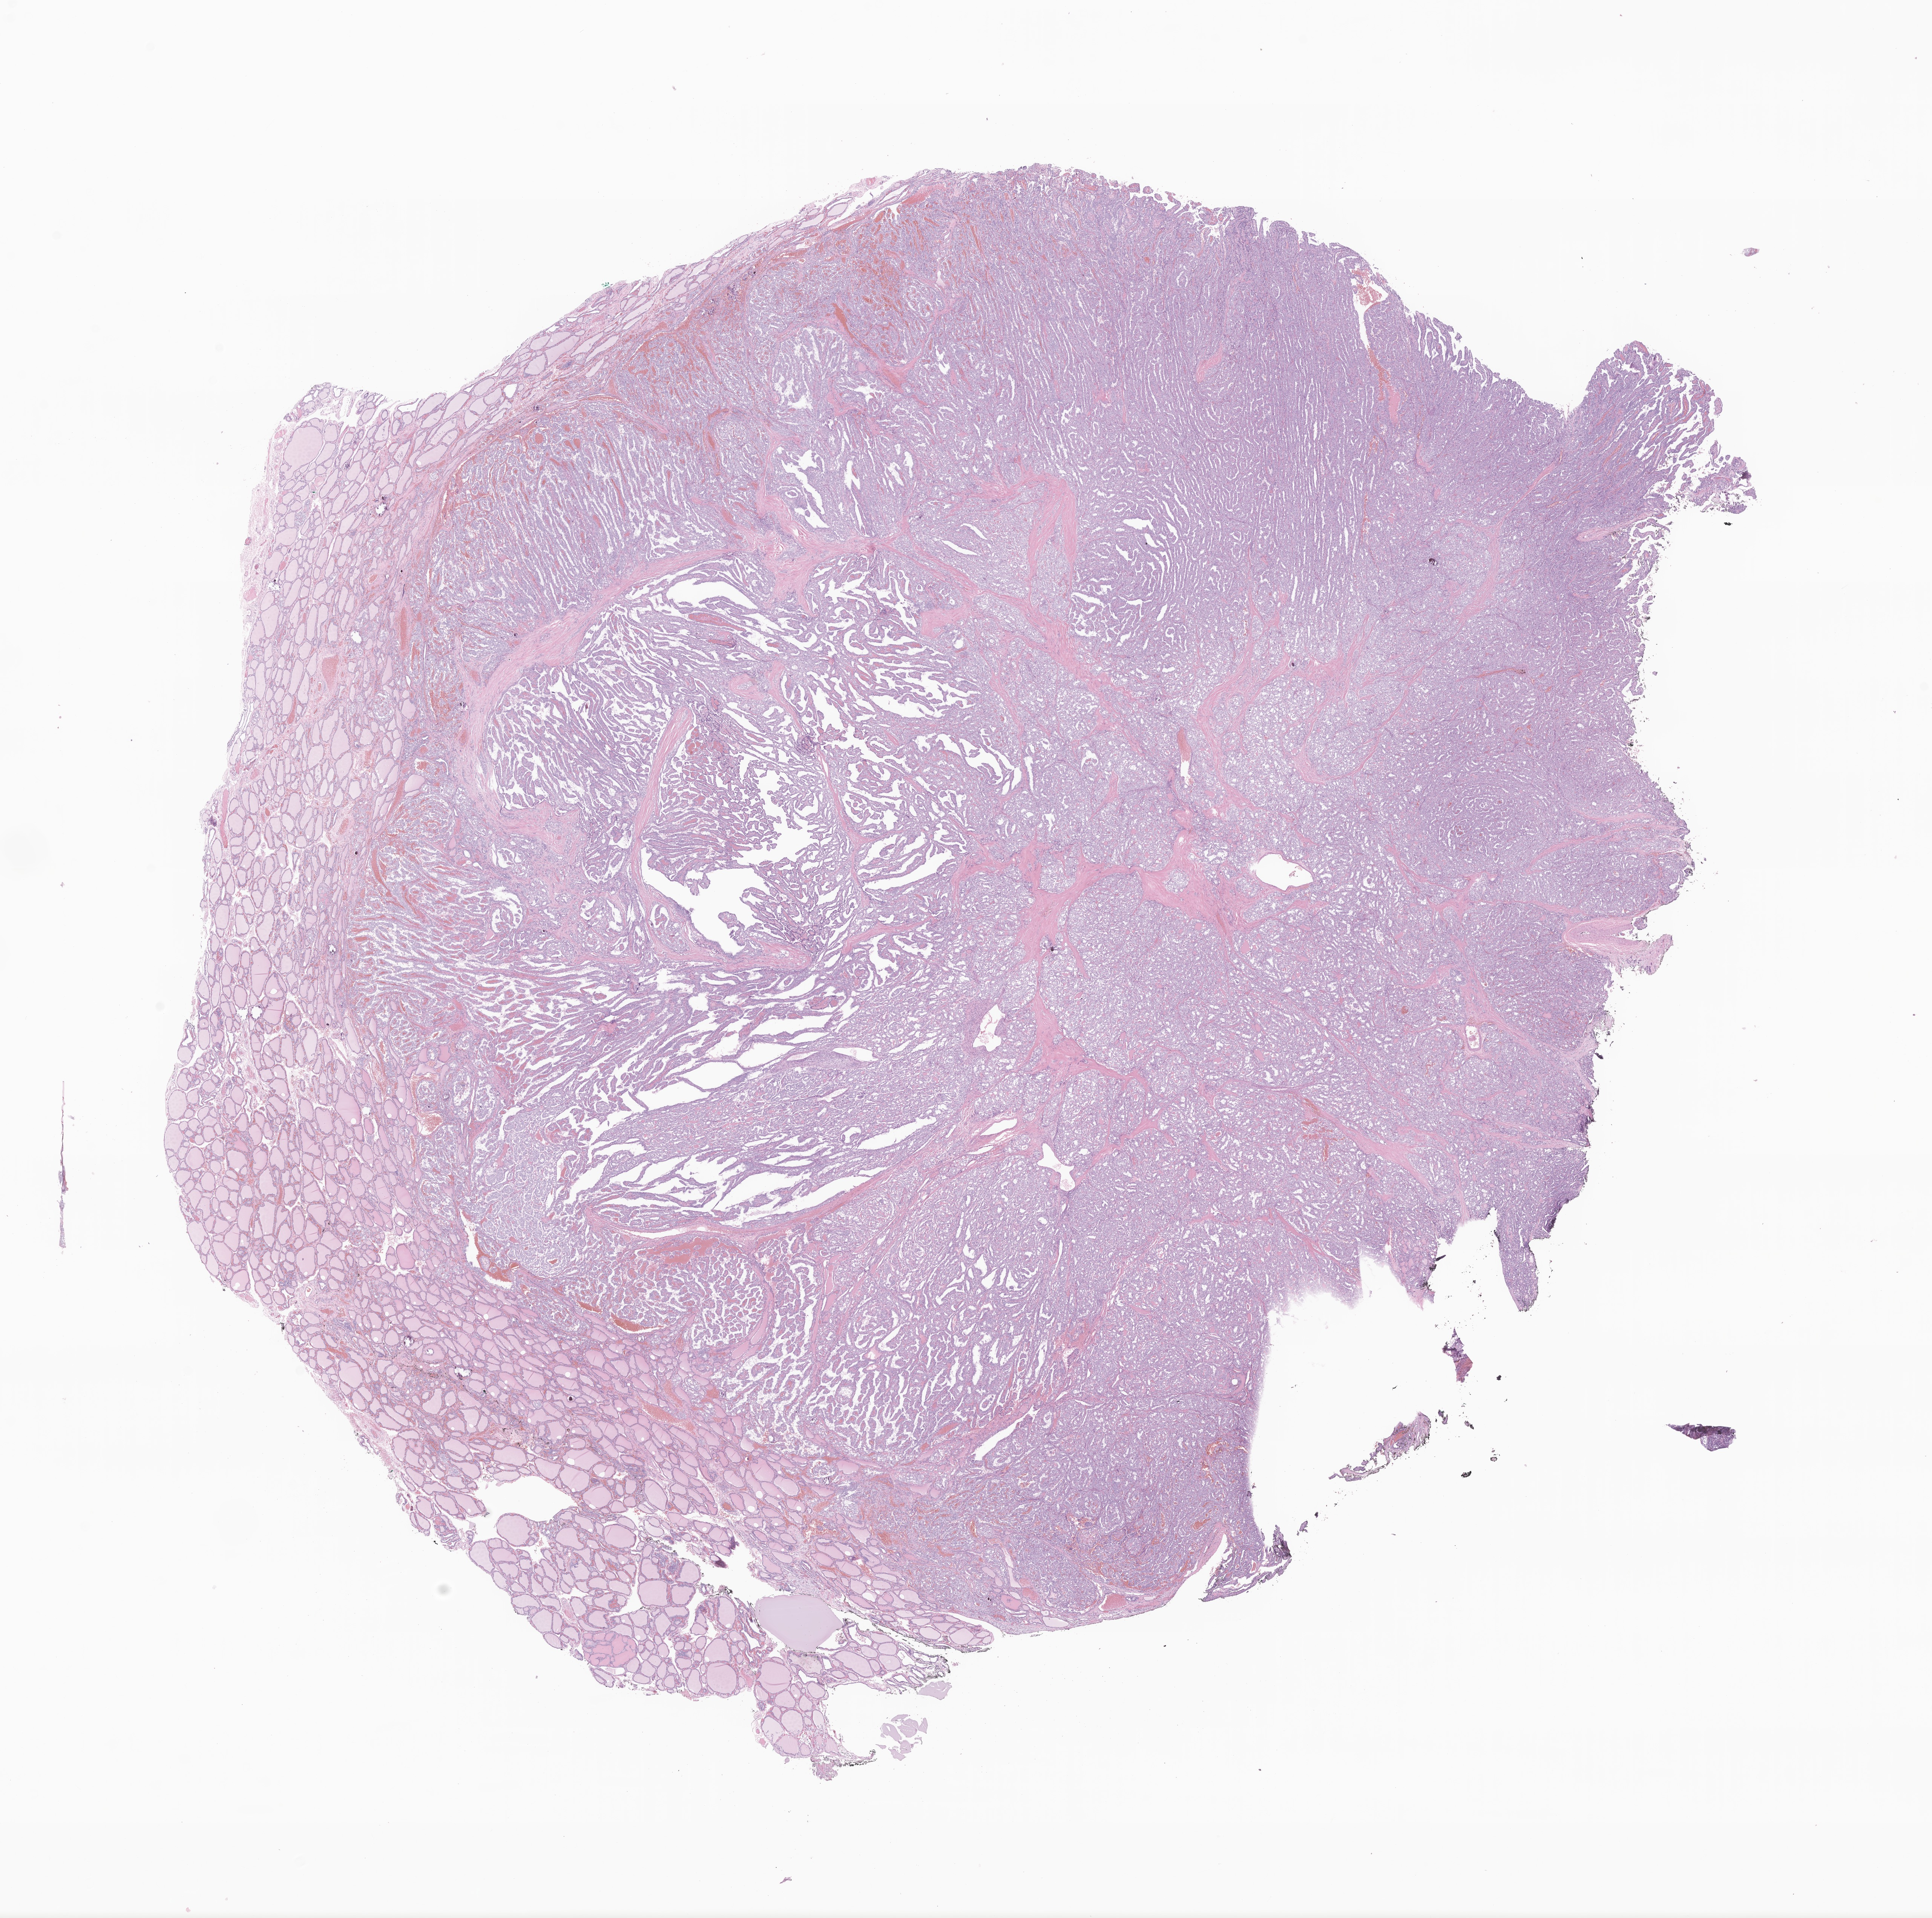
Haematoxylin and eosin whole-slide image of tumor tissue from the thyroid — whole scanned area (about 21.6 x 21.4 mm) shown as a low-resolution overview. Formalin-fixed paraffin-embedded section. Patient: male, age 104 months (8 years 8 months).
• diagnosis (ICD-O-3 morphology term): Papillary carcinoma, NOS